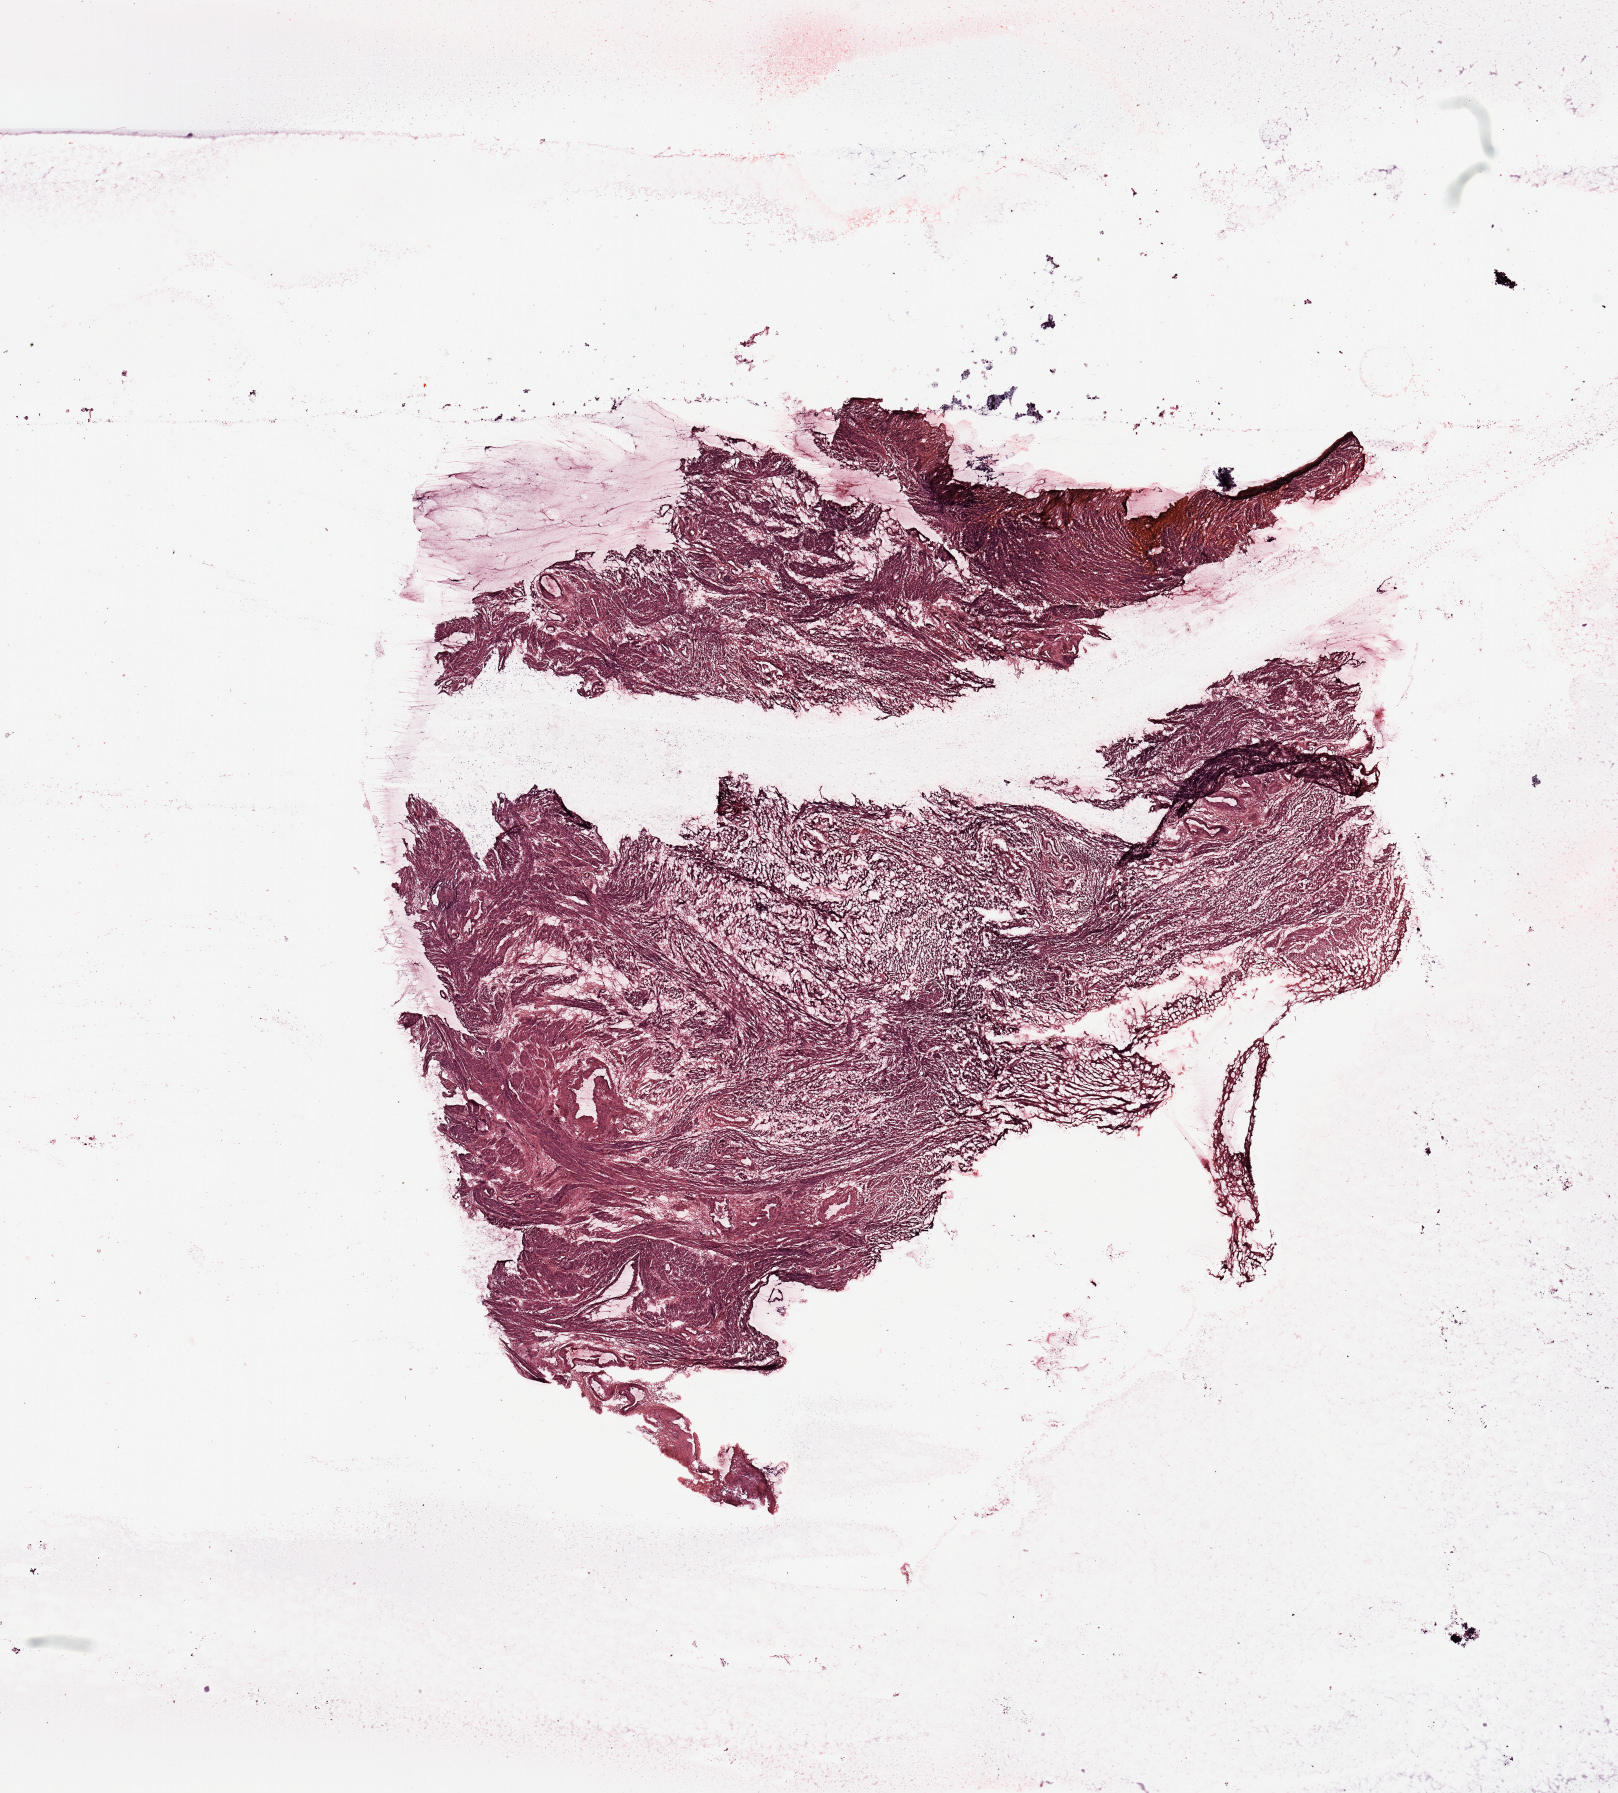
Digitized Hematoxylin and eosin (H&E) stained tissue section (whole slide), whole scanned area (about 12.8 x 14.2 mm) shown as a low-resolution overview, normal (non-tumour) tissue sample, uterus. Patient: female, age 67 years.
This section: normal (non-tumour) tissue from the same patient. Patient diagnosis: Endometrioid adenocarcinoma, NOS.